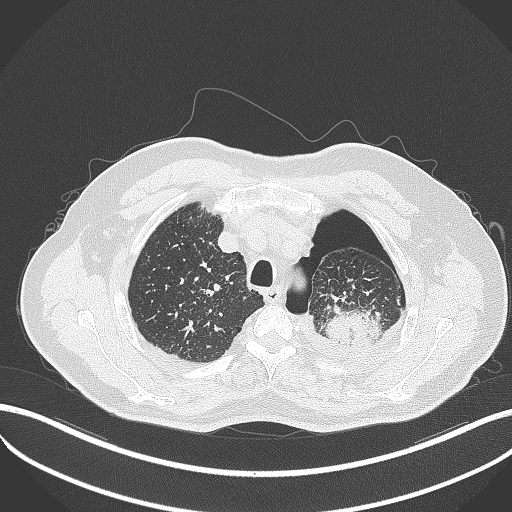
Chest CT, one axial slice; slice 412 of 464 in the series (ordered by position); reconstruction kernel B70f; lung window (W 1500 / L -600 HU); 512 × 512 image matrix, field of view 400 × 400 mm. Male patient, age 76 years. From the clinical record (not read from this slice): clinical TNM (as recorded): T3 N0 M1b.
Outlined on this slice (bounding box drawn by a radiologist):
- lung tumour (recorded histology: adenocarcinoma): bounding box (x1, y1, x2, y2) in pixels: (323, 298, 381, 344)